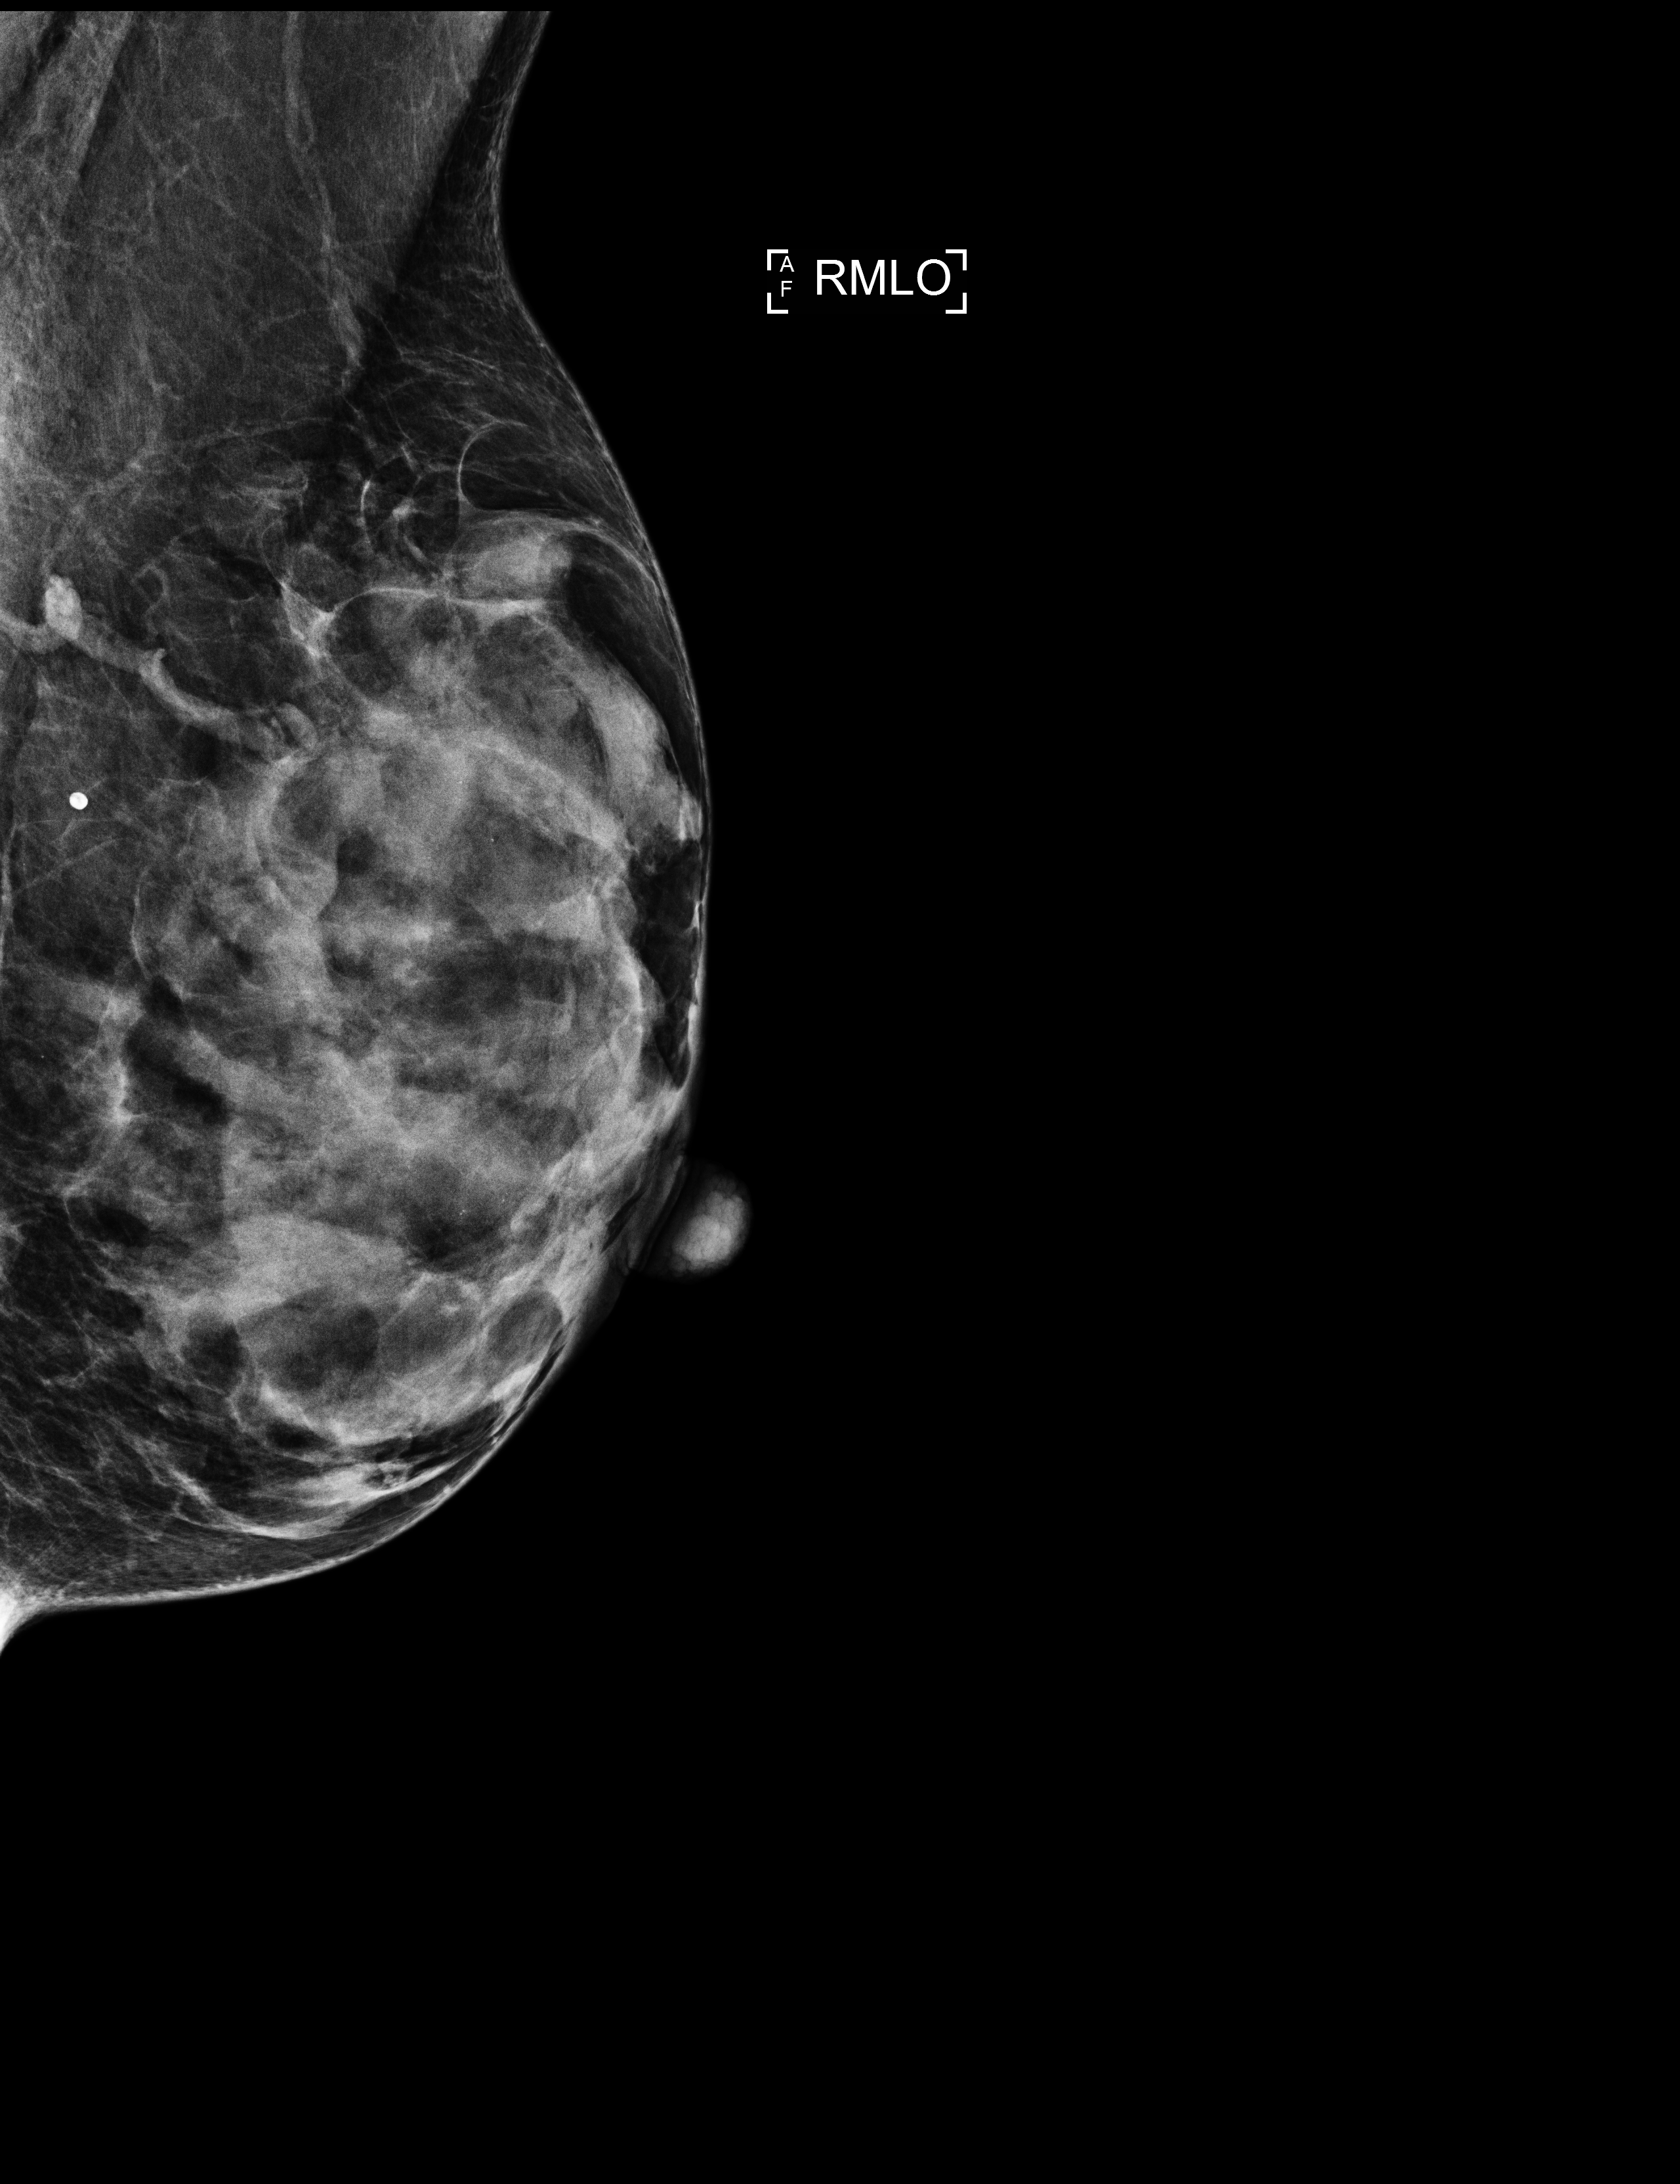
Digital mammogram (FFDM); right breast; medio-lateral oblique projection; screening examination. Patient aged 53 years (female).
- breast density at the screening exam (both breasts): heterogeneously dense (BI-RADS density category c)
- final BI-RADS category for the screening round (tomosynthesis exam, both breasts): category 1
- recall: no recall after this screen